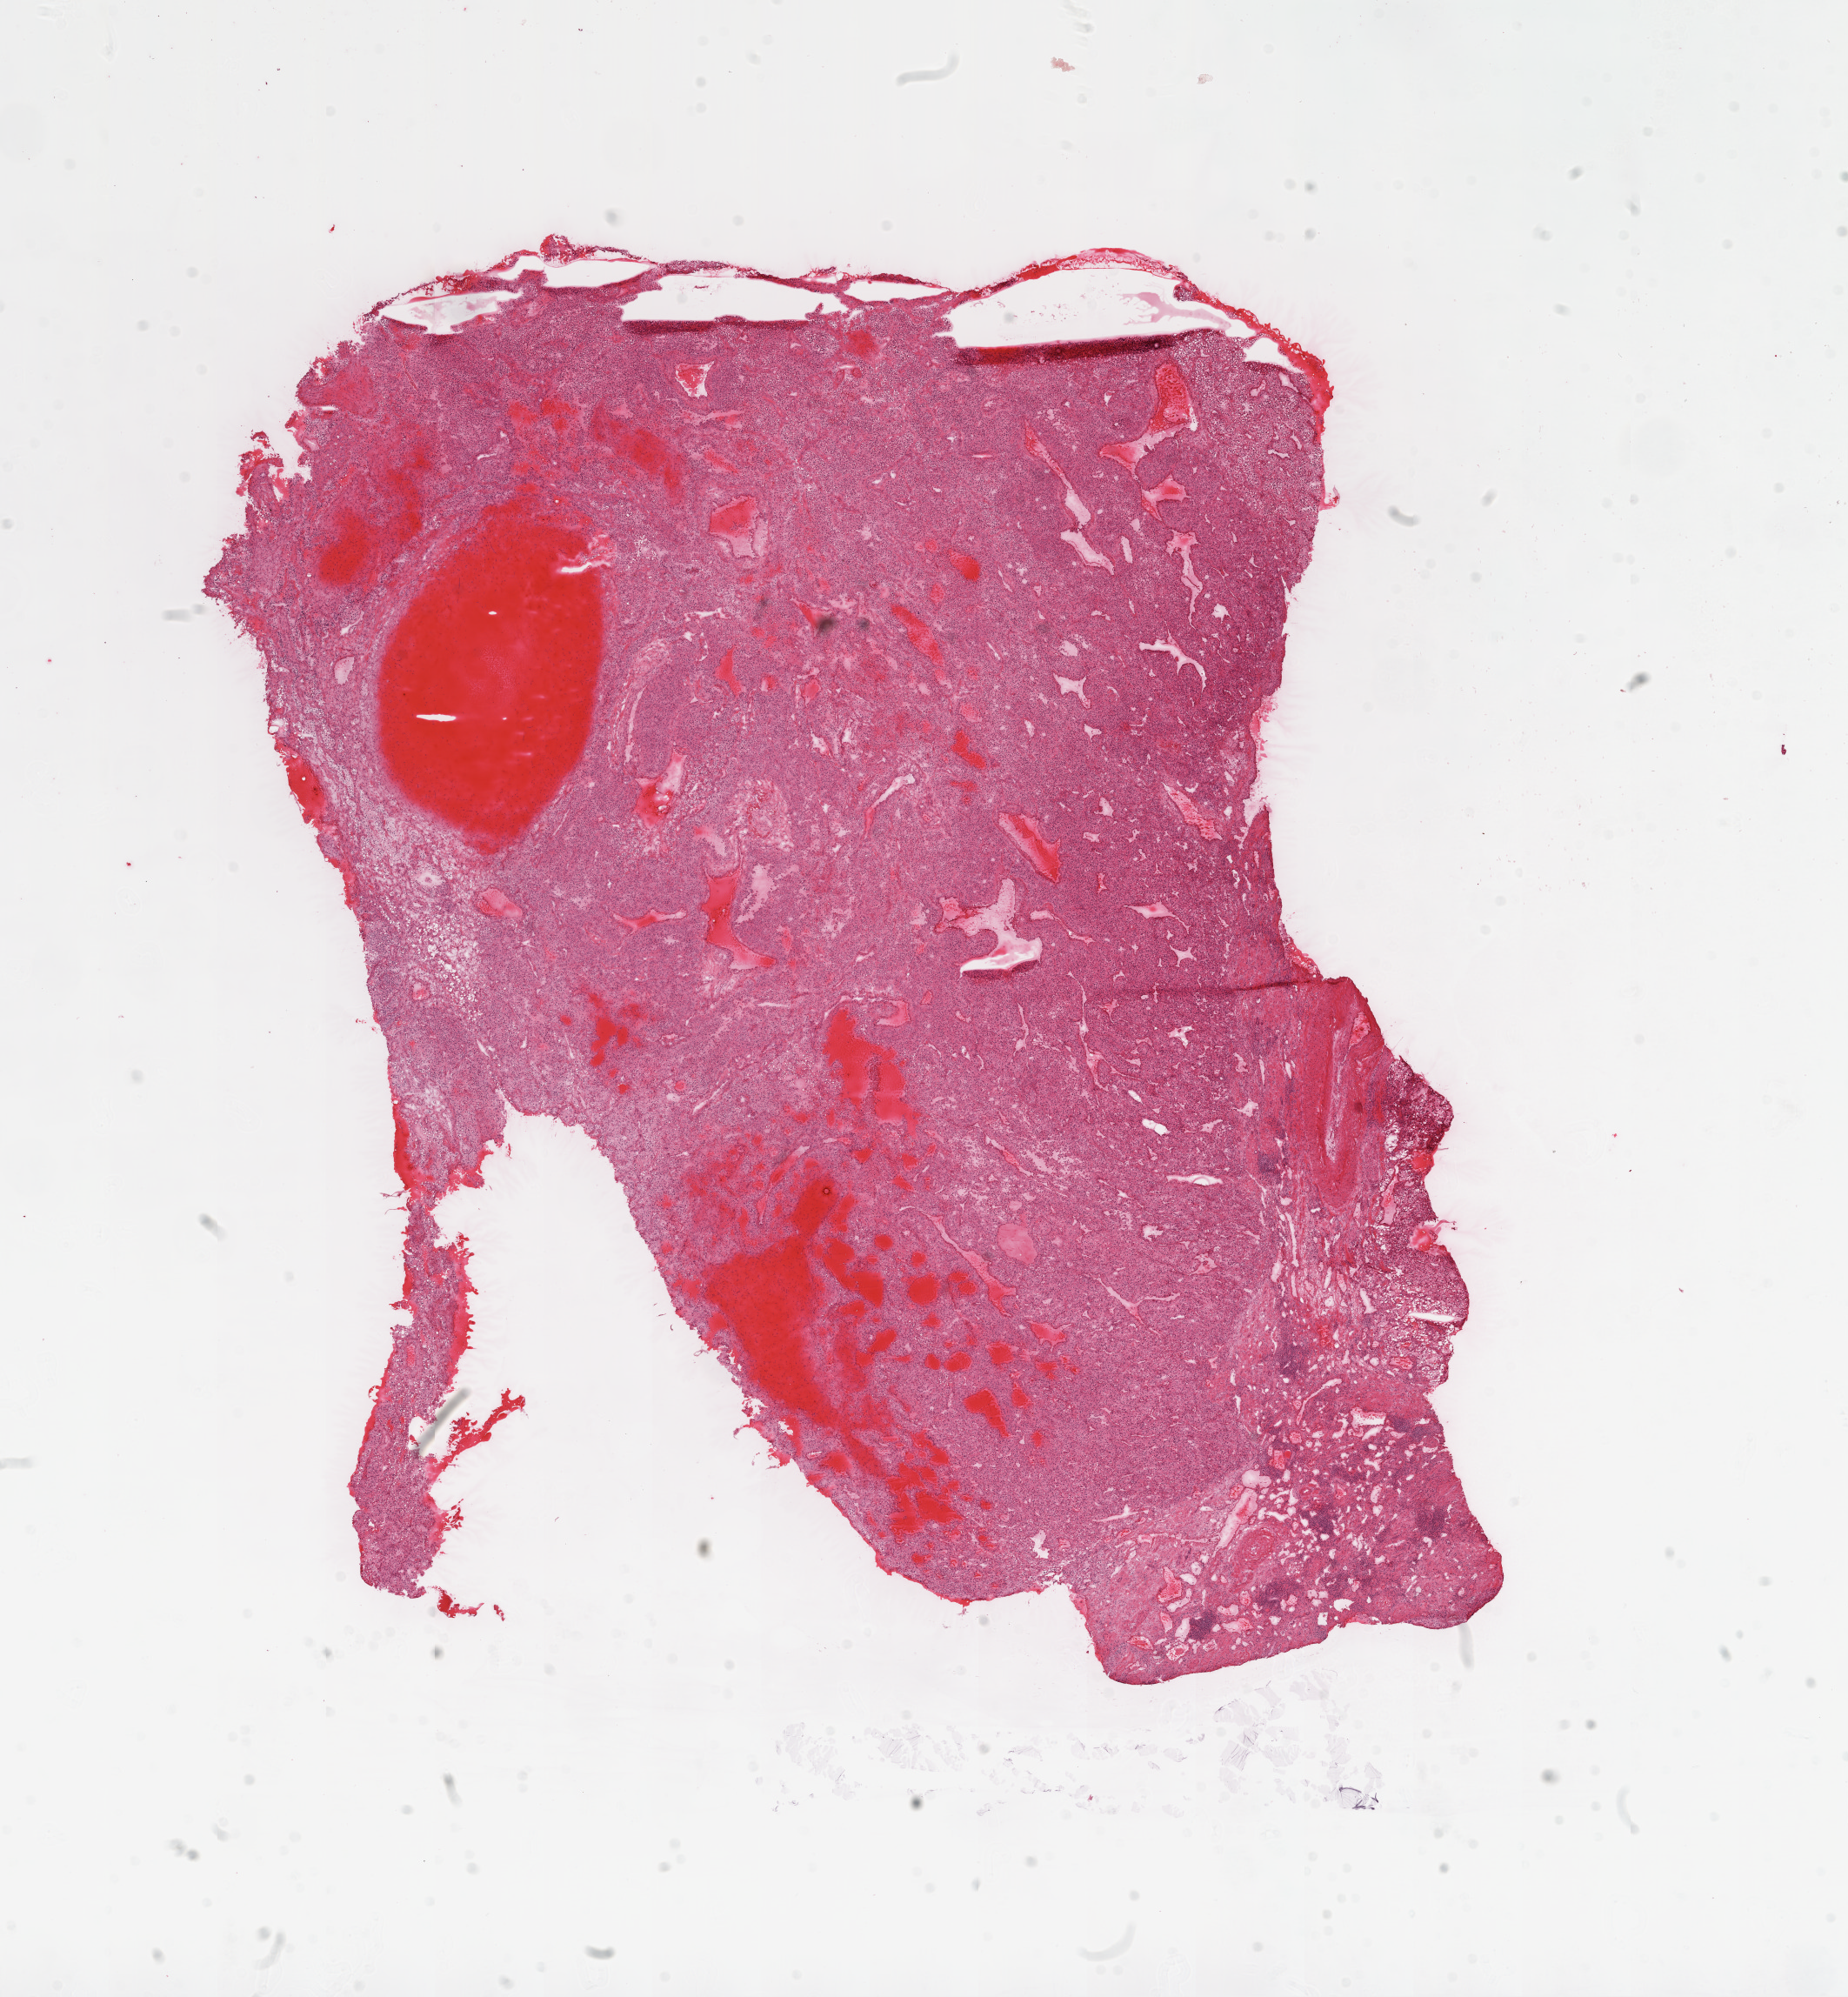
Whole-slide histology image, H&E — a low-resolution overview of the entire scanned area, about 17.1 x 18.4 mm; frozen section from the top of the tissue portion; primary tumour sample from the kidney. Patient: male, age at initial diagnosis 79 years. Histologic grade: G3 (poorly differentiated). Slide review estimates, as recorded: tumour cells 80%, tumour nuclei 70%, normal cells 0%, stromal cells 20%, necrosis 0%.
AJCC pathologic stage: II. Diagnosis: Clear cell adenocarcinoma, NOS.